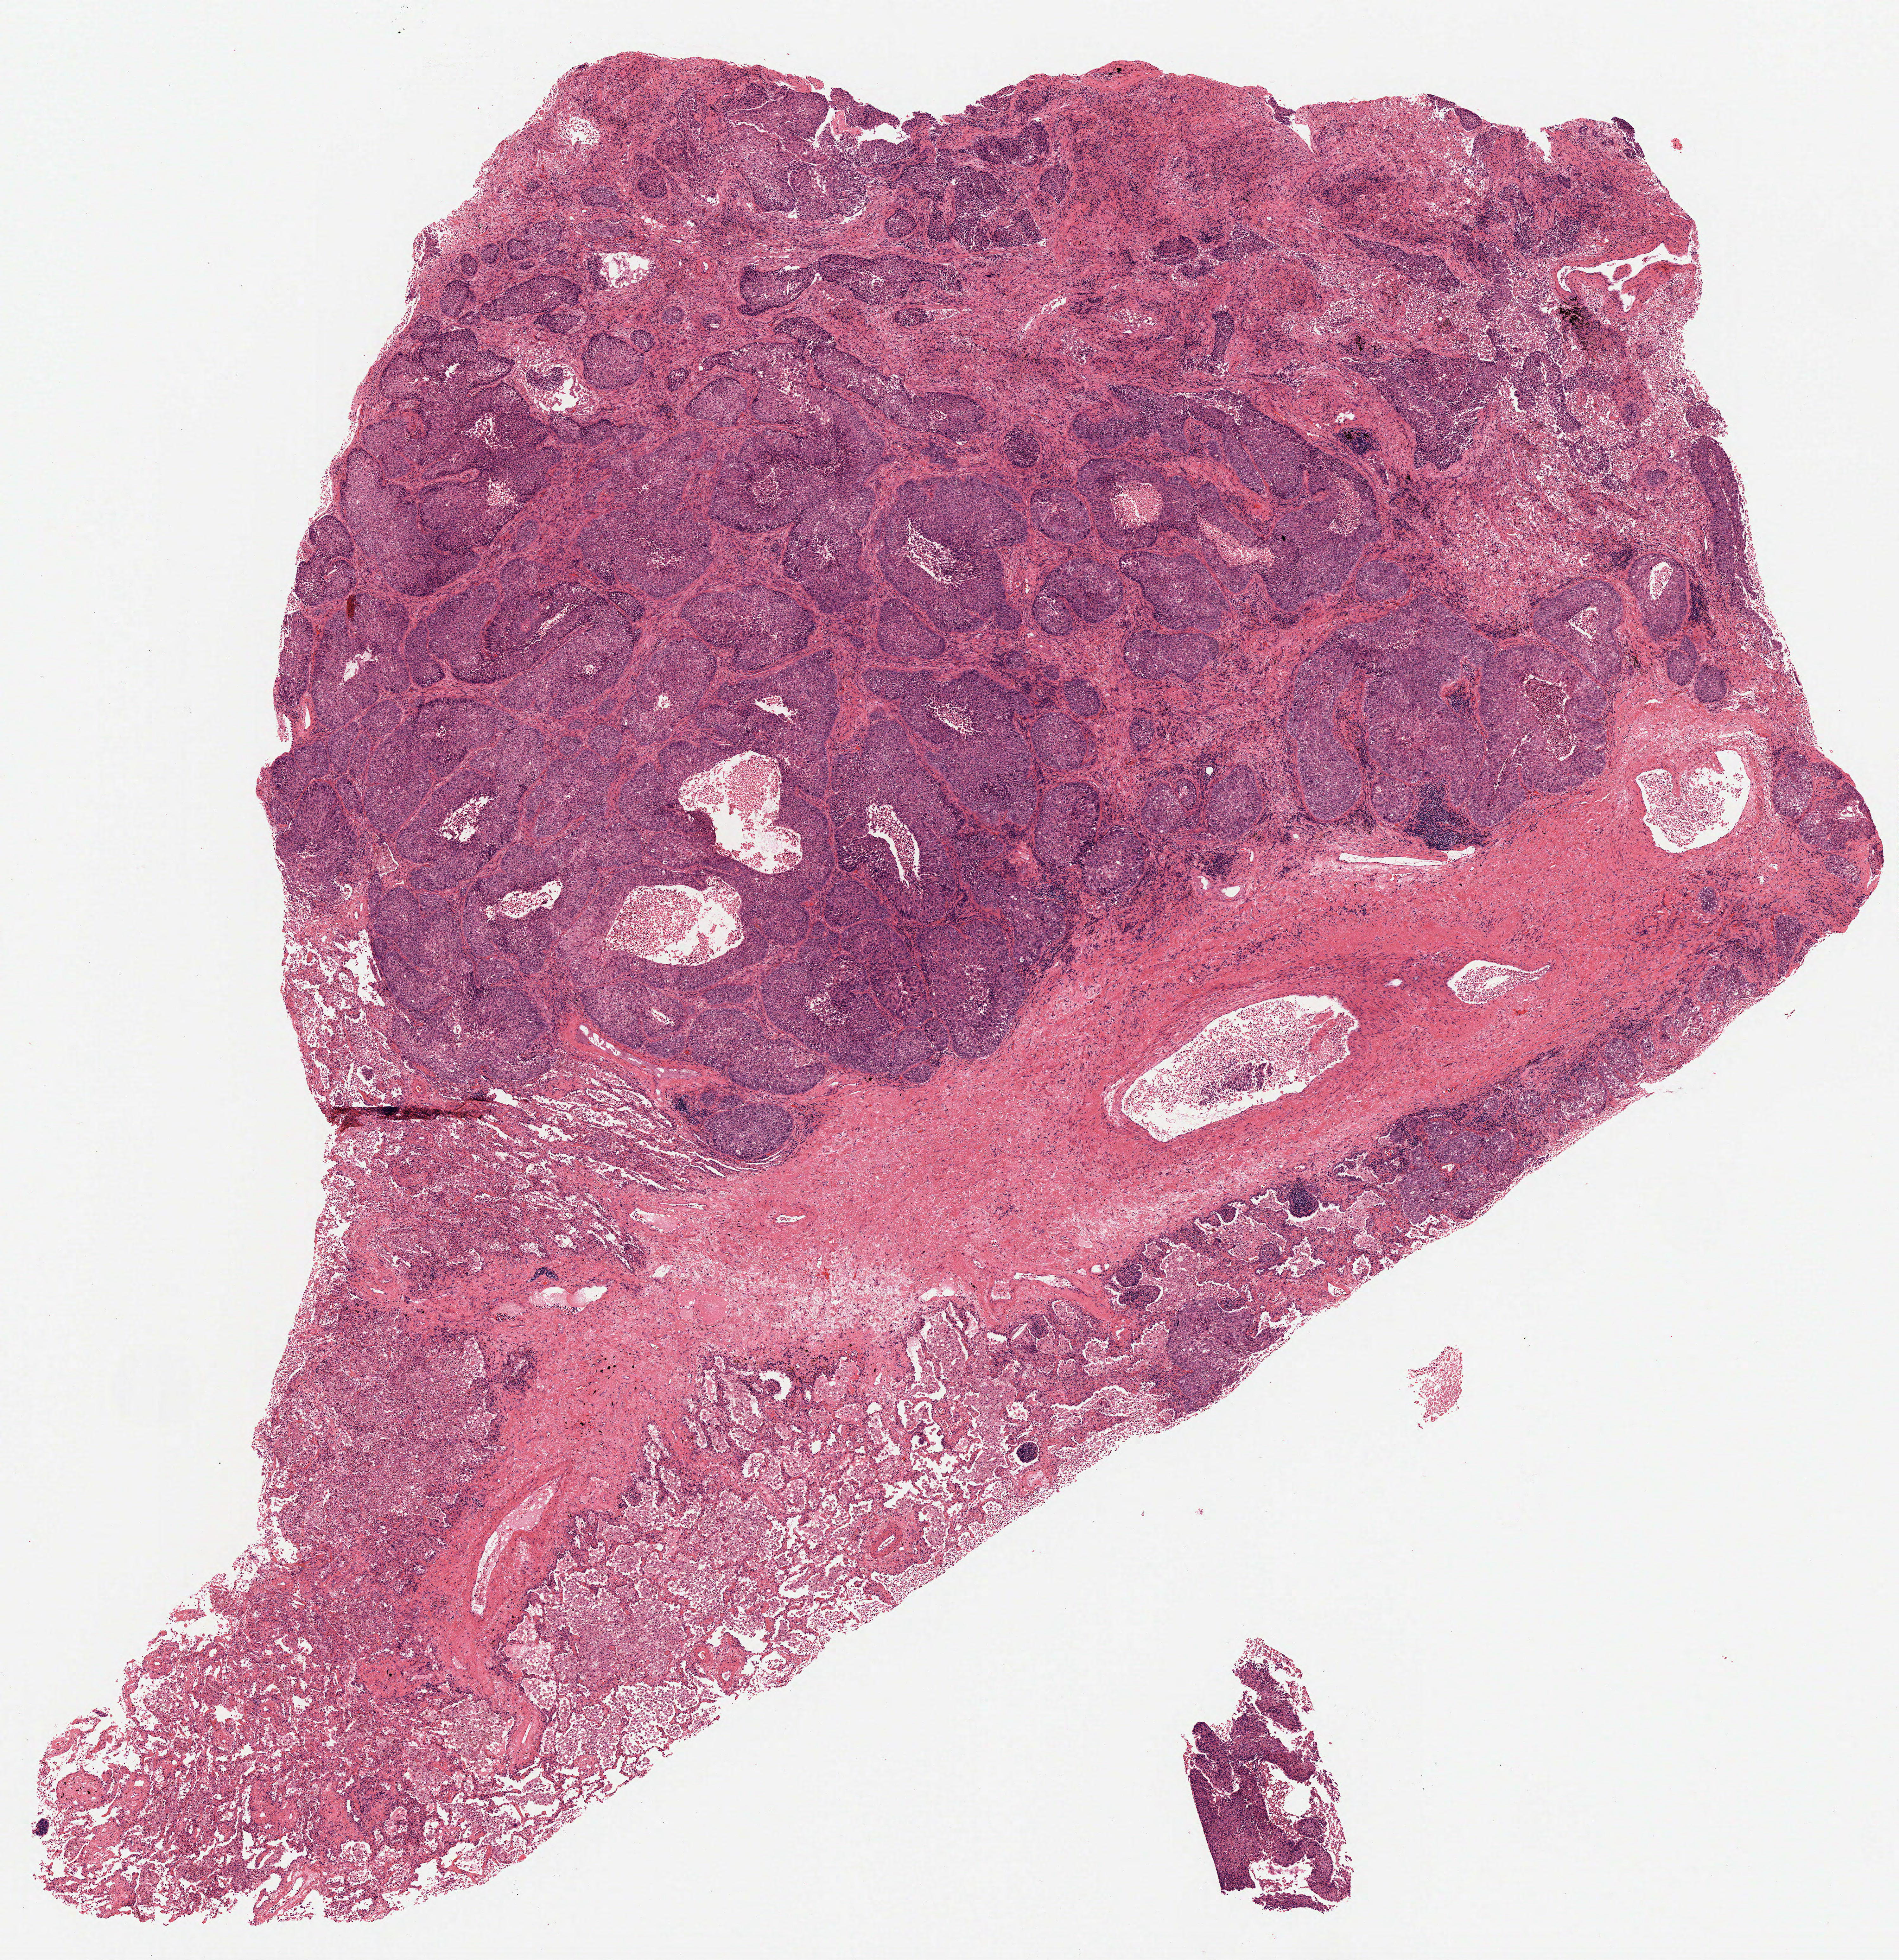
Digitized H&E tissue section (whole slide) — a low-resolution overview of the entire scanned area, about 12.0 x 12.4 mm (from a 20x scan); FFPE section; lung, primary tumour sample. Patient sex: male.
- pathologic diagnosis: Squamous cell carcinoma, NOS
- AJCC pathologic stage: IIB (6th edition)